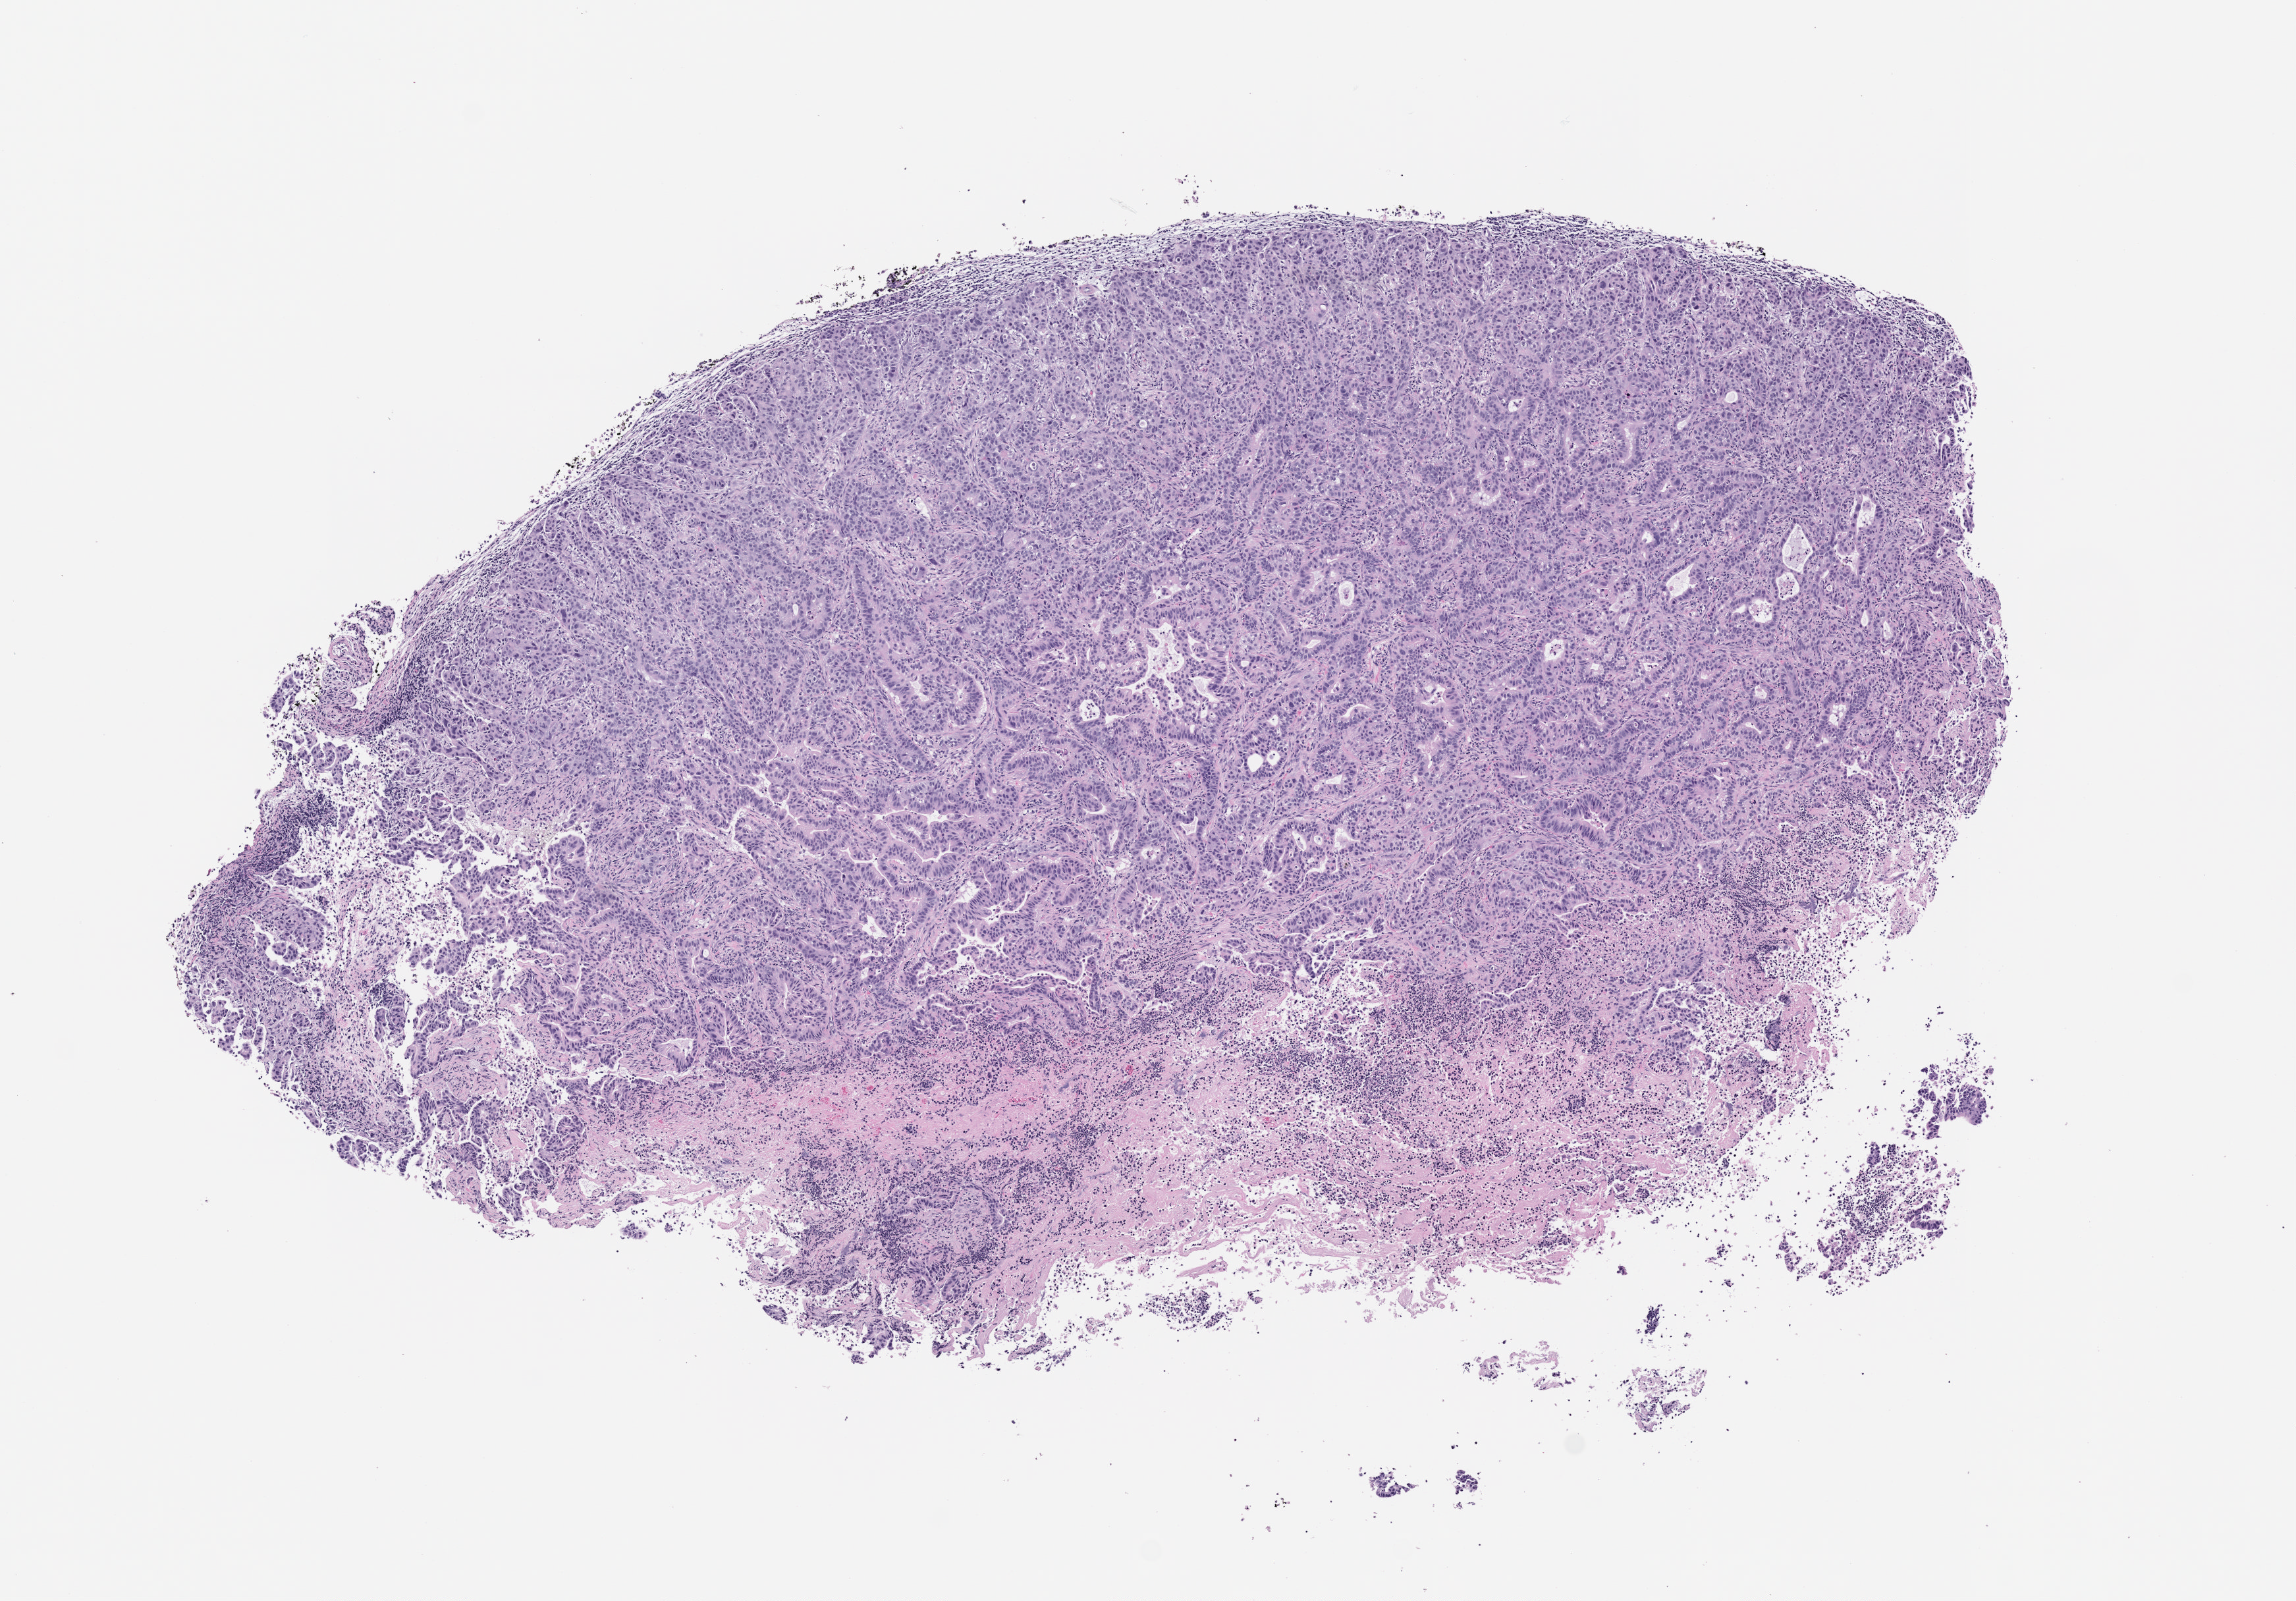
Haematoxylin and eosin whole-slide image of a patient-derived xenograft (PDX) tumor grown in a mouse, passage 1, low-resolution overview of the scanned area, about 7.0 x 4.9 mm, formalin-fixed paraffin-embedded section, originating tumor site category: pancreas.
- originating patient diagnosis: Pancreatic Adenocarcinoma